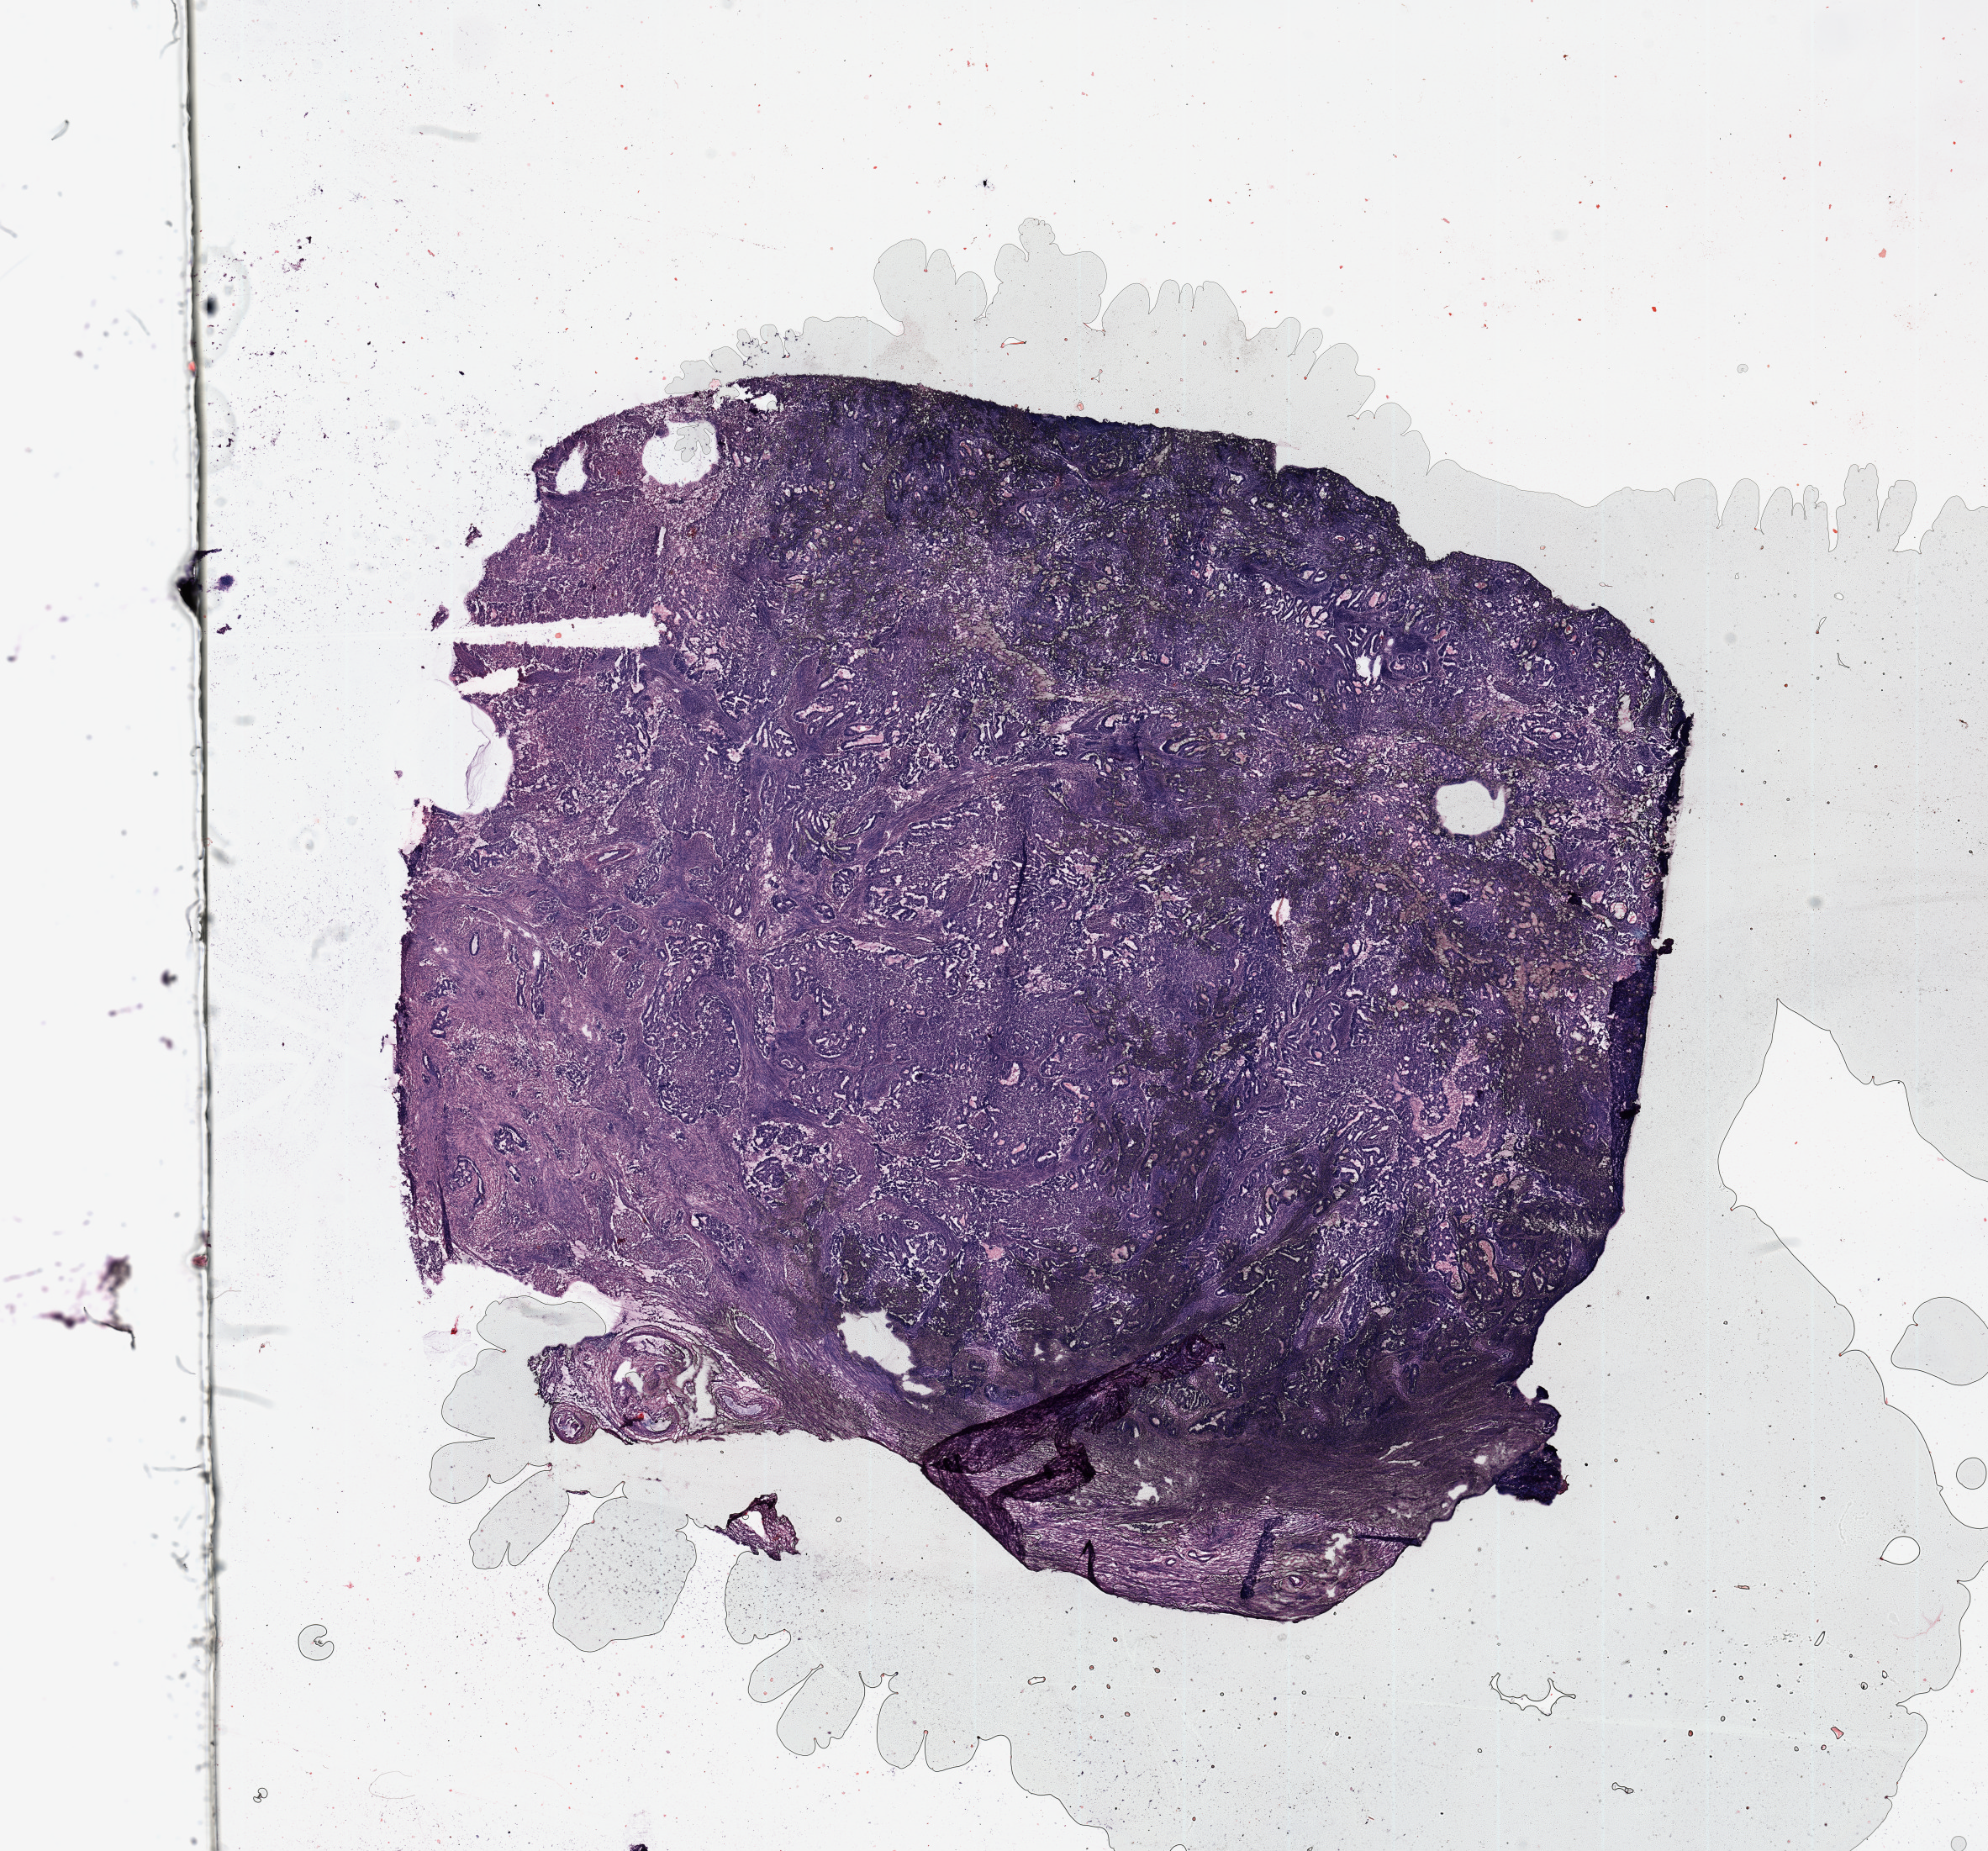
H&E whole-slide image, a low-resolution overview of the entire scanned area, about 18.7 x 17.4 mm (acquisition: 20x scan). Uterus, tumour tissue. Patient: female, age 62 years. Histologic grade: G2 (moderately differentiated).
* histologic diagnosis: Endometrioid adenocarcinoma, NOS
* AJCC pathologic stage: I